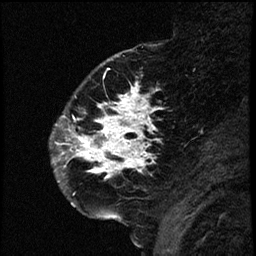
Breast MRI (dynamic contrast-enhanced), one sagittal slice; slice 19 of 66 in the series (ordered by position); dynamic contrast-enhanced study with each time point stored as its own series, time point 2 of 3 at this slice position (early post-contrast, ordered by acquisition time); 1.5 T; TE 4.2 ms, TR 17.6 ms; 2 mm slice thickness; 256 × 256 image matrix, field of view 200 × 200 mm. Female patient. Case-level facts recorded for this patient, not image findings: setting: breast cancer imaged before/during neoadjuvant chemotherapy; receptor status: HER2-positive.
Structures marked on this image (semi-automatically segmented with operator editing):
- analysis volume of interest (the breast-tissue region the enhancement analysis was run in; not a lesion): bounding box (x1, y1, x2, y2) in pixels: (53, 69, 177, 209)
- tumour enhancement mask (voxels above the 100 % enhancement threshold inside the analysis volume of interest): (55, 87, 158, 178)